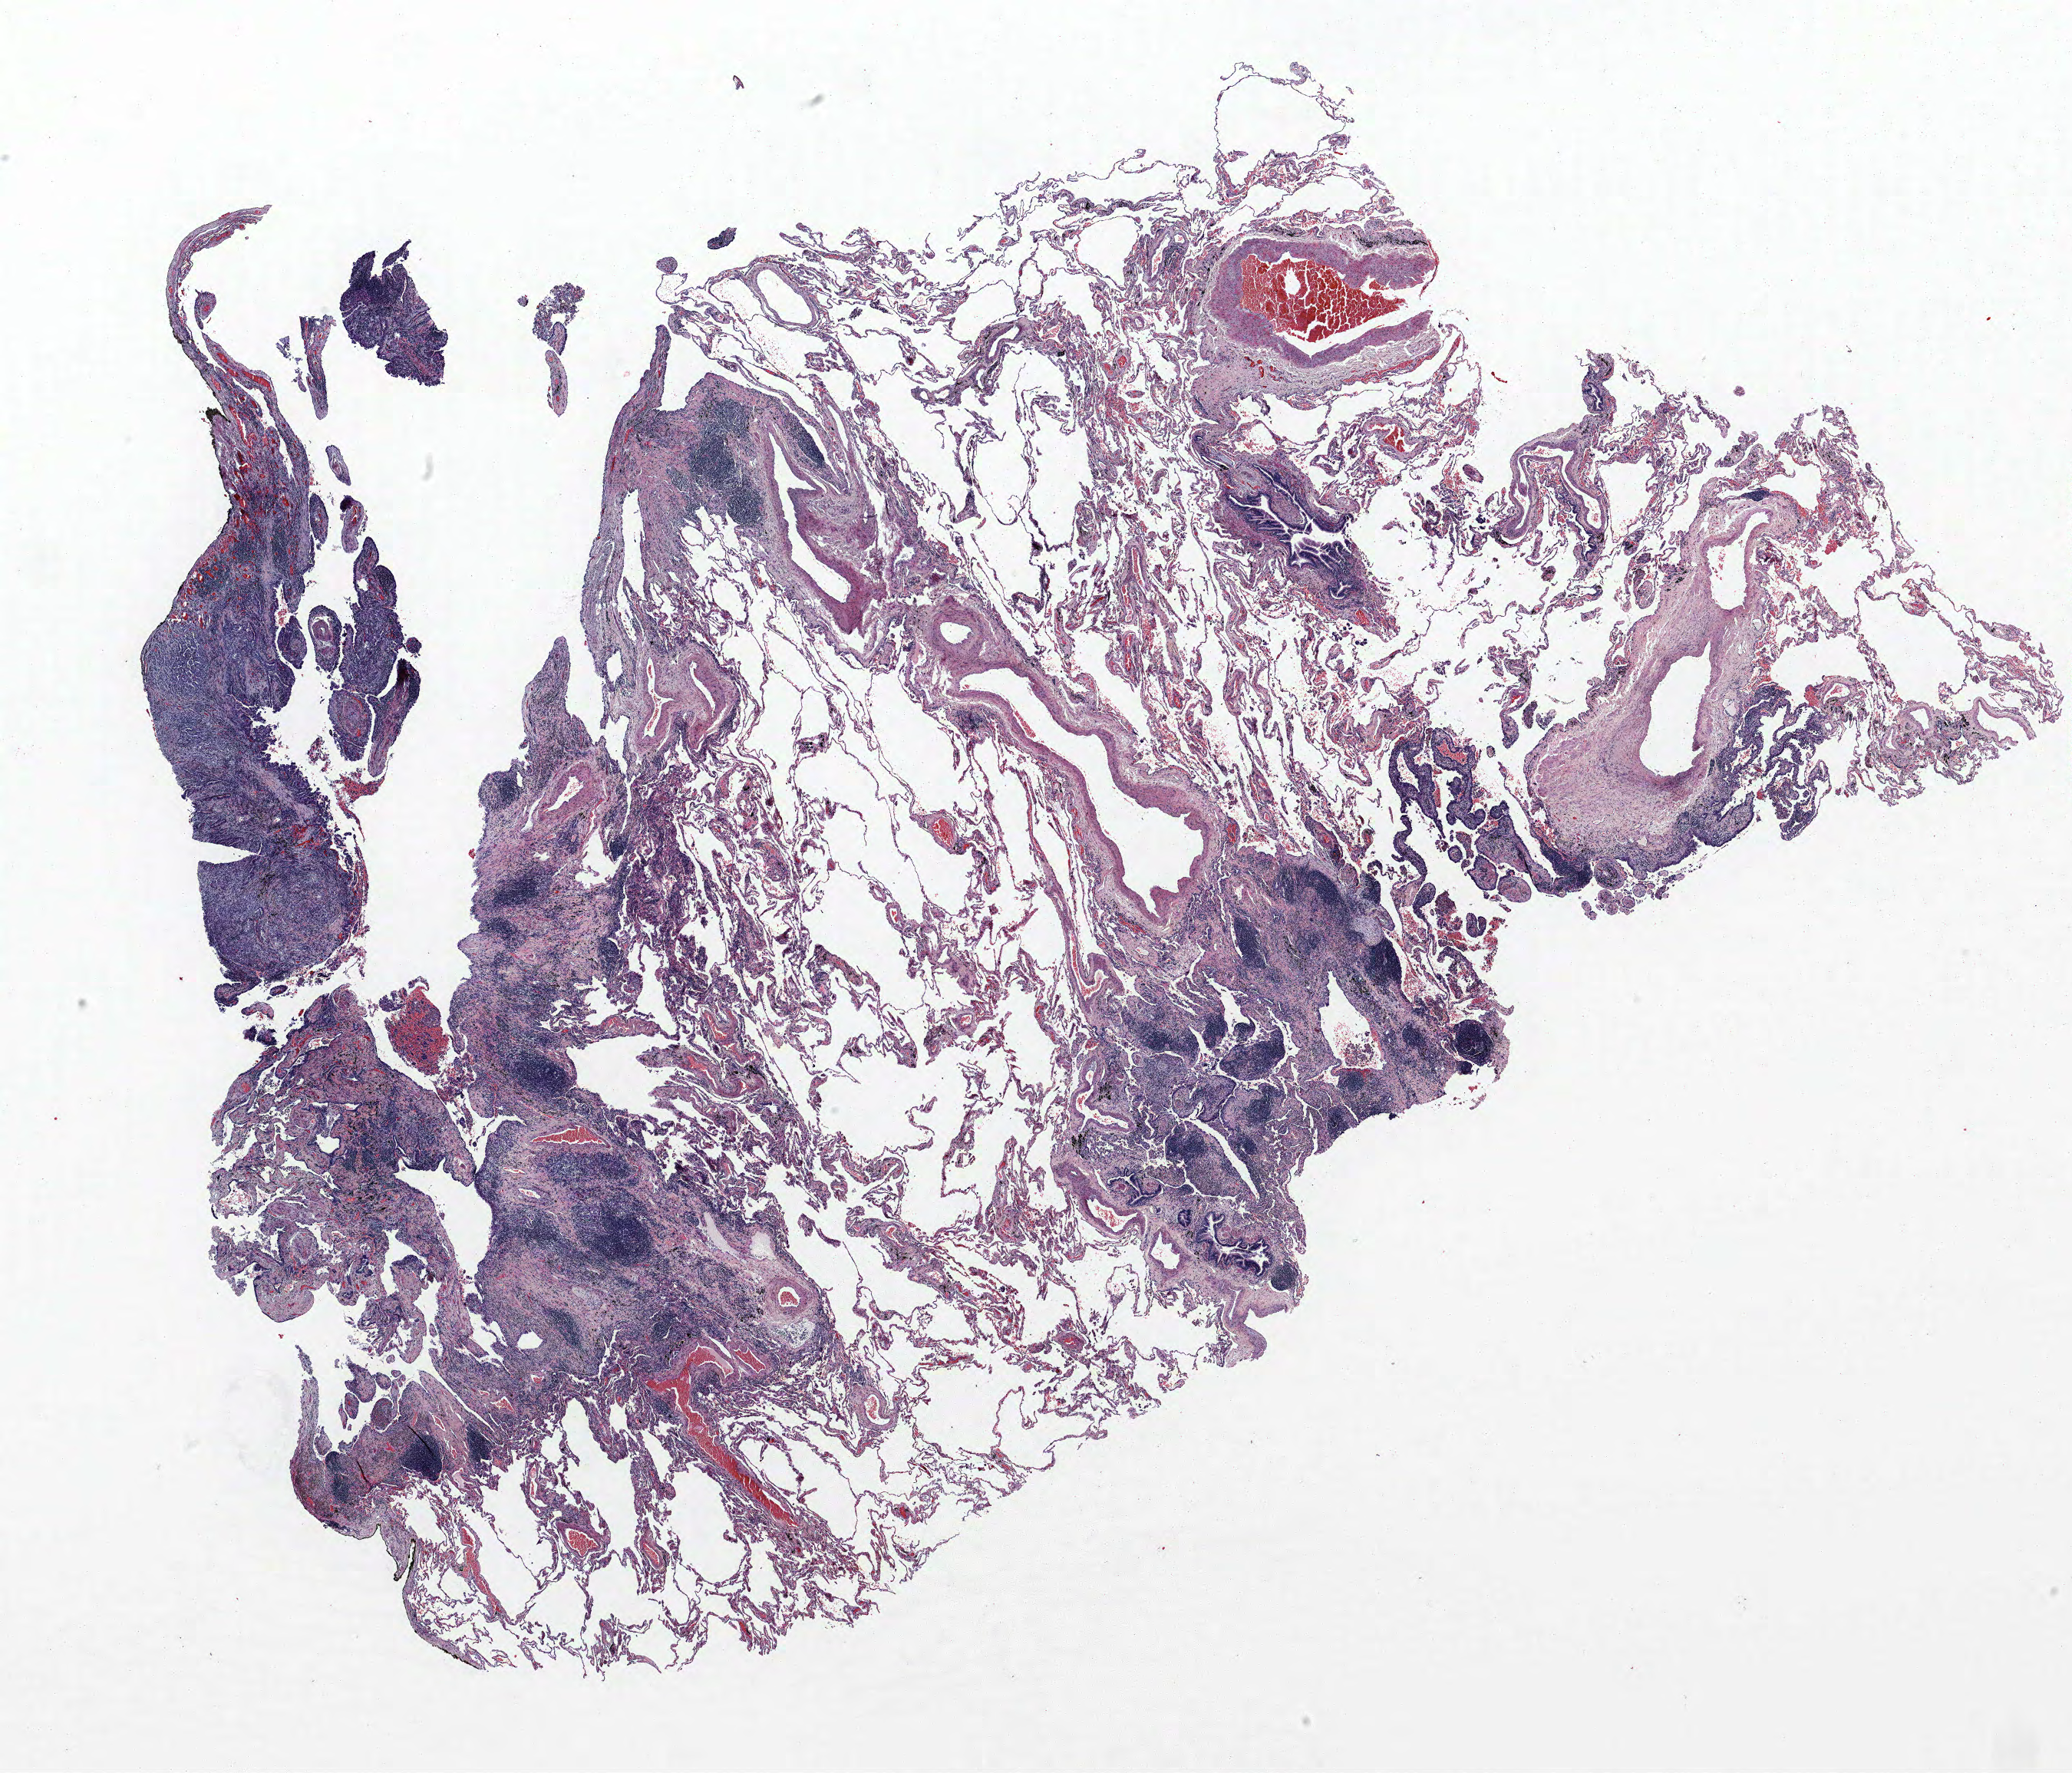
H&E whole-slide image, shown as a low-resolution overview of the whole scanned area (about 21.6 x 18.5 mm, acquisition: 40x scan), formalin-fixed paraffin-embedded (FFPE) section, lung tissue. Female patient, aged 60 at enrolment. Current smoker at enrolment. Grade: well differentiated (G1).
* primary tumour location (clinical record): left lower lobe
* stage (AJCC 6th edition): IA
* participant's lung-cancer diagnosis: Adenocarcinoma, NOS
* tumour size (pathology): 15 mm